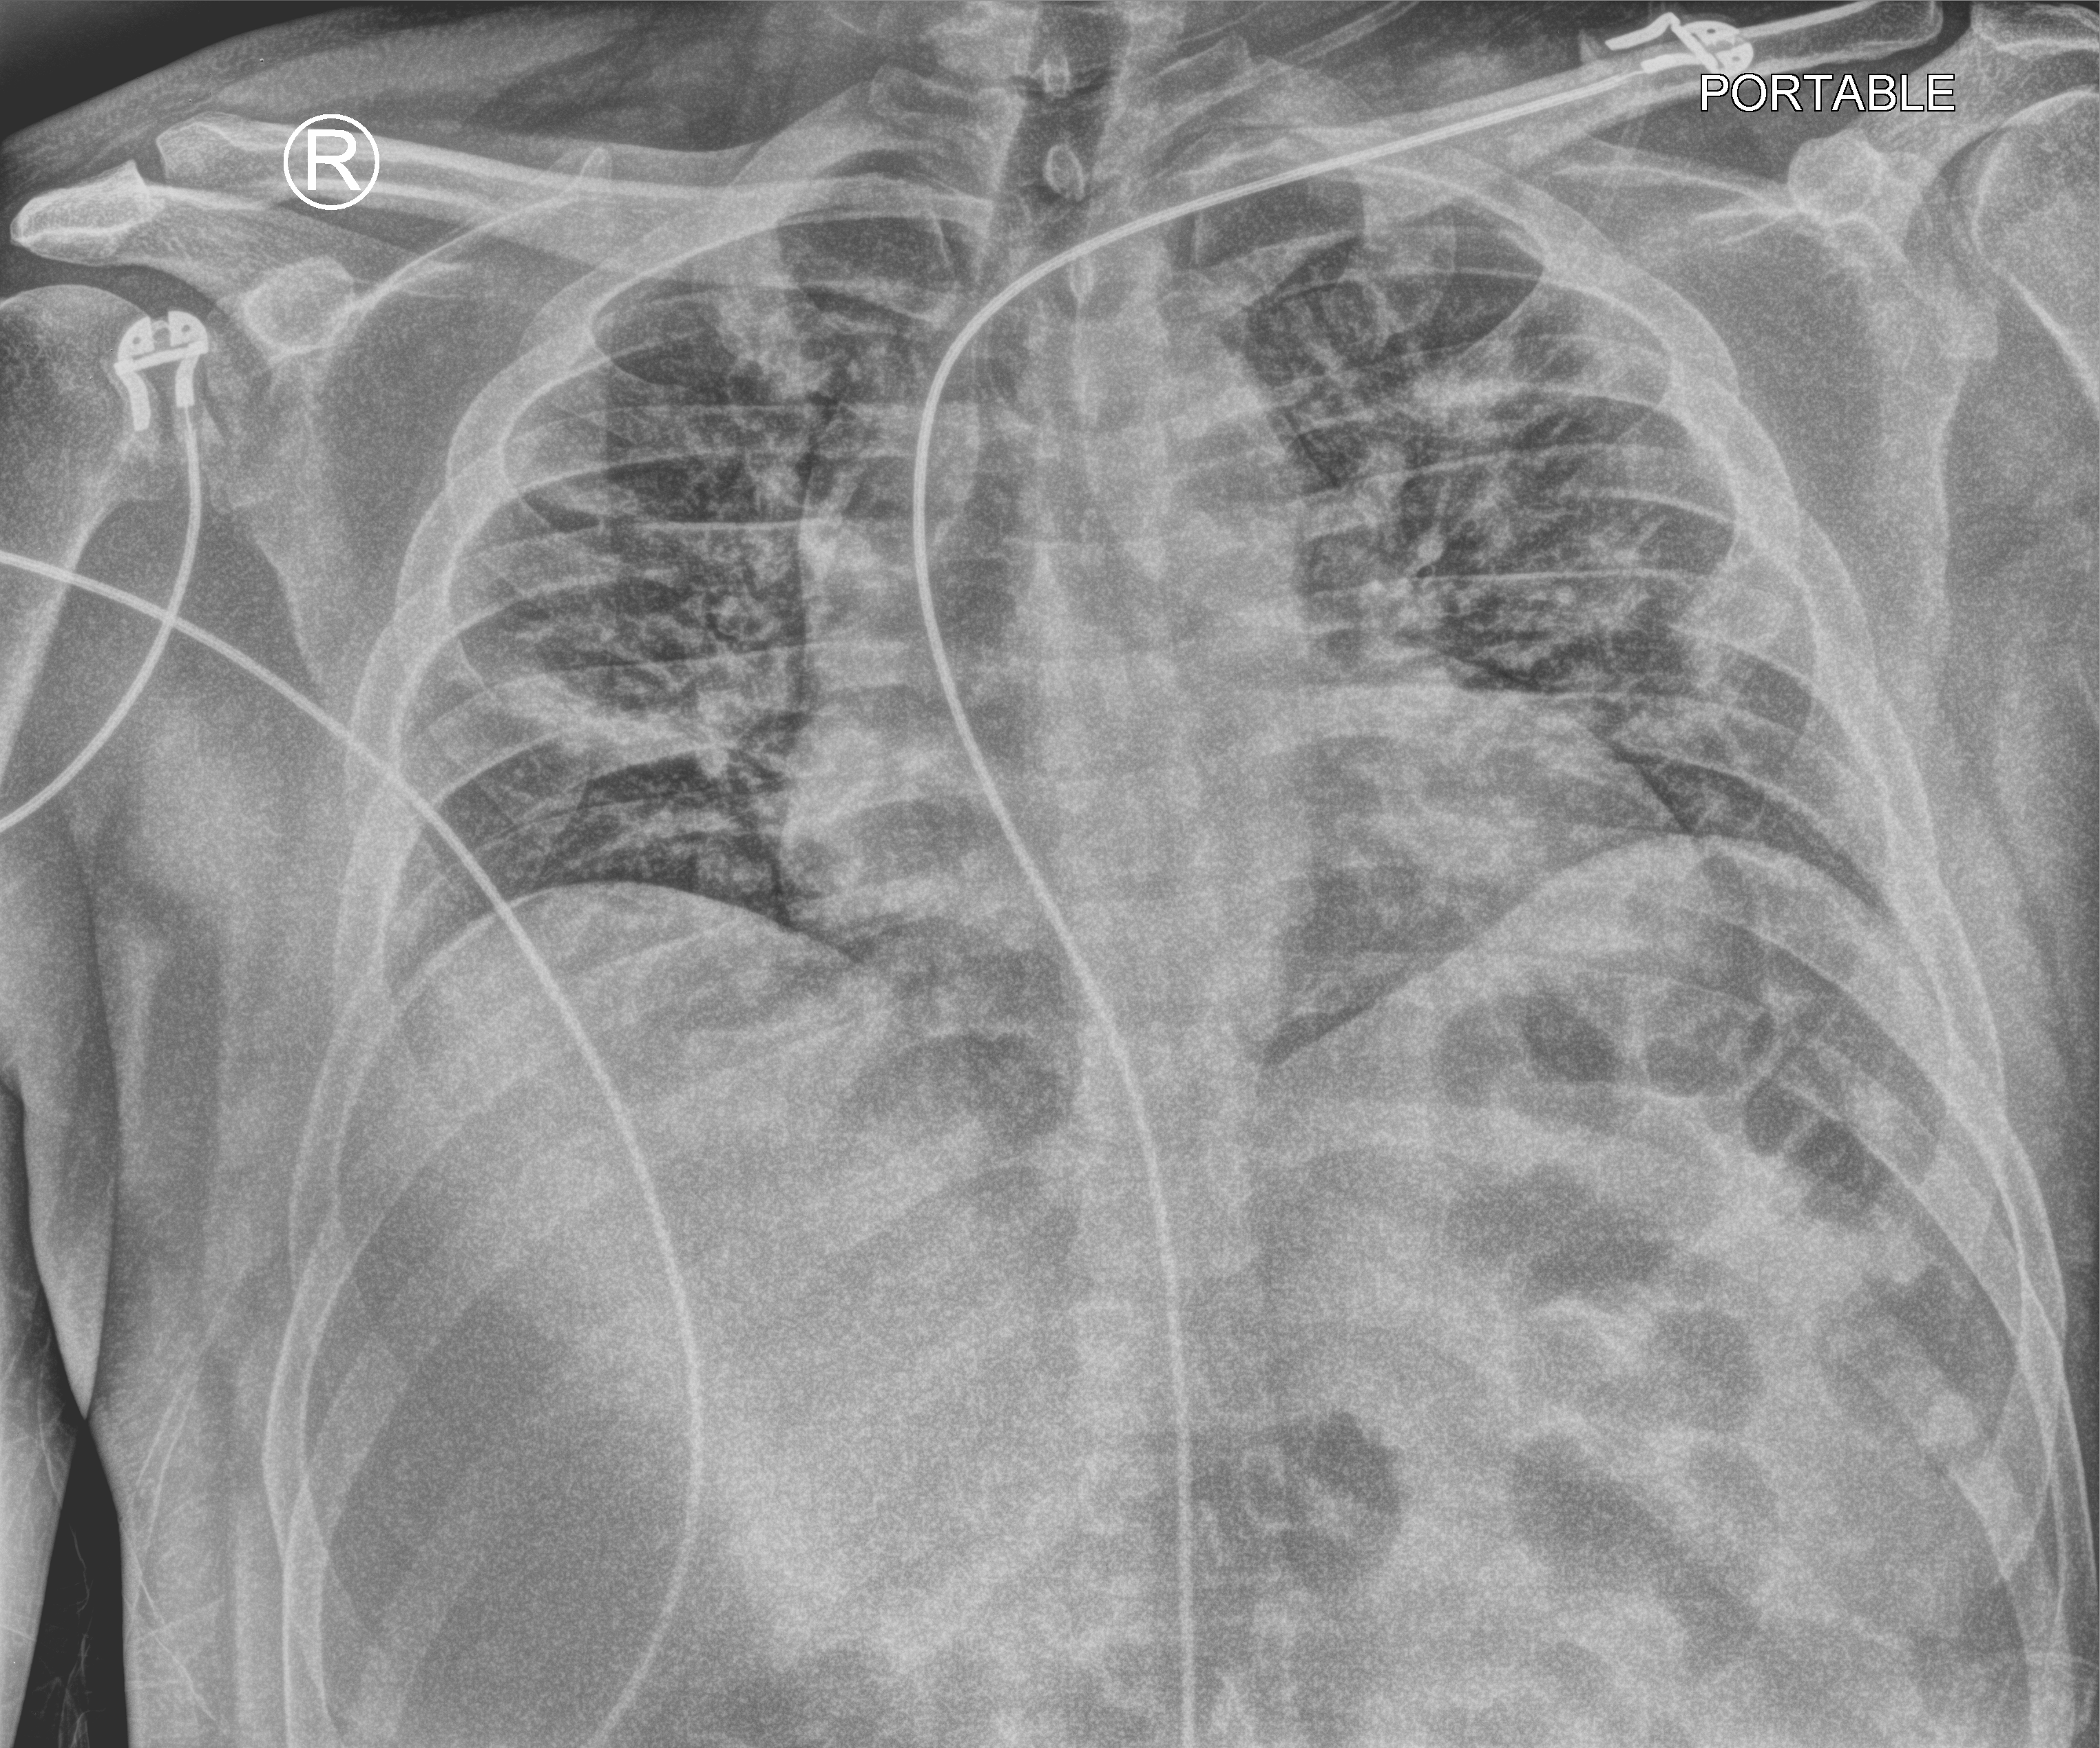
Chest X-ray (portable). Male patient hospitalised with COVID-19, age 18–59 years.
Hospital-stay facts (about this admission, not read from this image; timing relative to this image not recorded): admitted to intensive care during this hospital stay: no; other chronic lung disease (admission record): no; mechanically ventilated during this hospital stay: no.